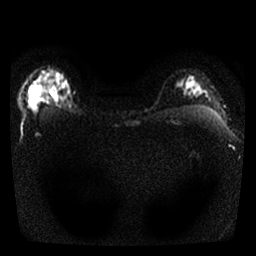
Breast MRI, one axial slice. Diffusion-weighted series; image 2 of 4 stored at this slice position (different b-values; order by instance number). 1.5 T. 4 mm slice thickness. 256 × 256 image matrix, field of view 300 × 300 mm. Female patient.
Structures marked on this image (outlined manually by an expert reader):
- tumour on diffusion-weighted imaging: bounding box <28,85,64,103> (left, top, right, bottom; pixels)